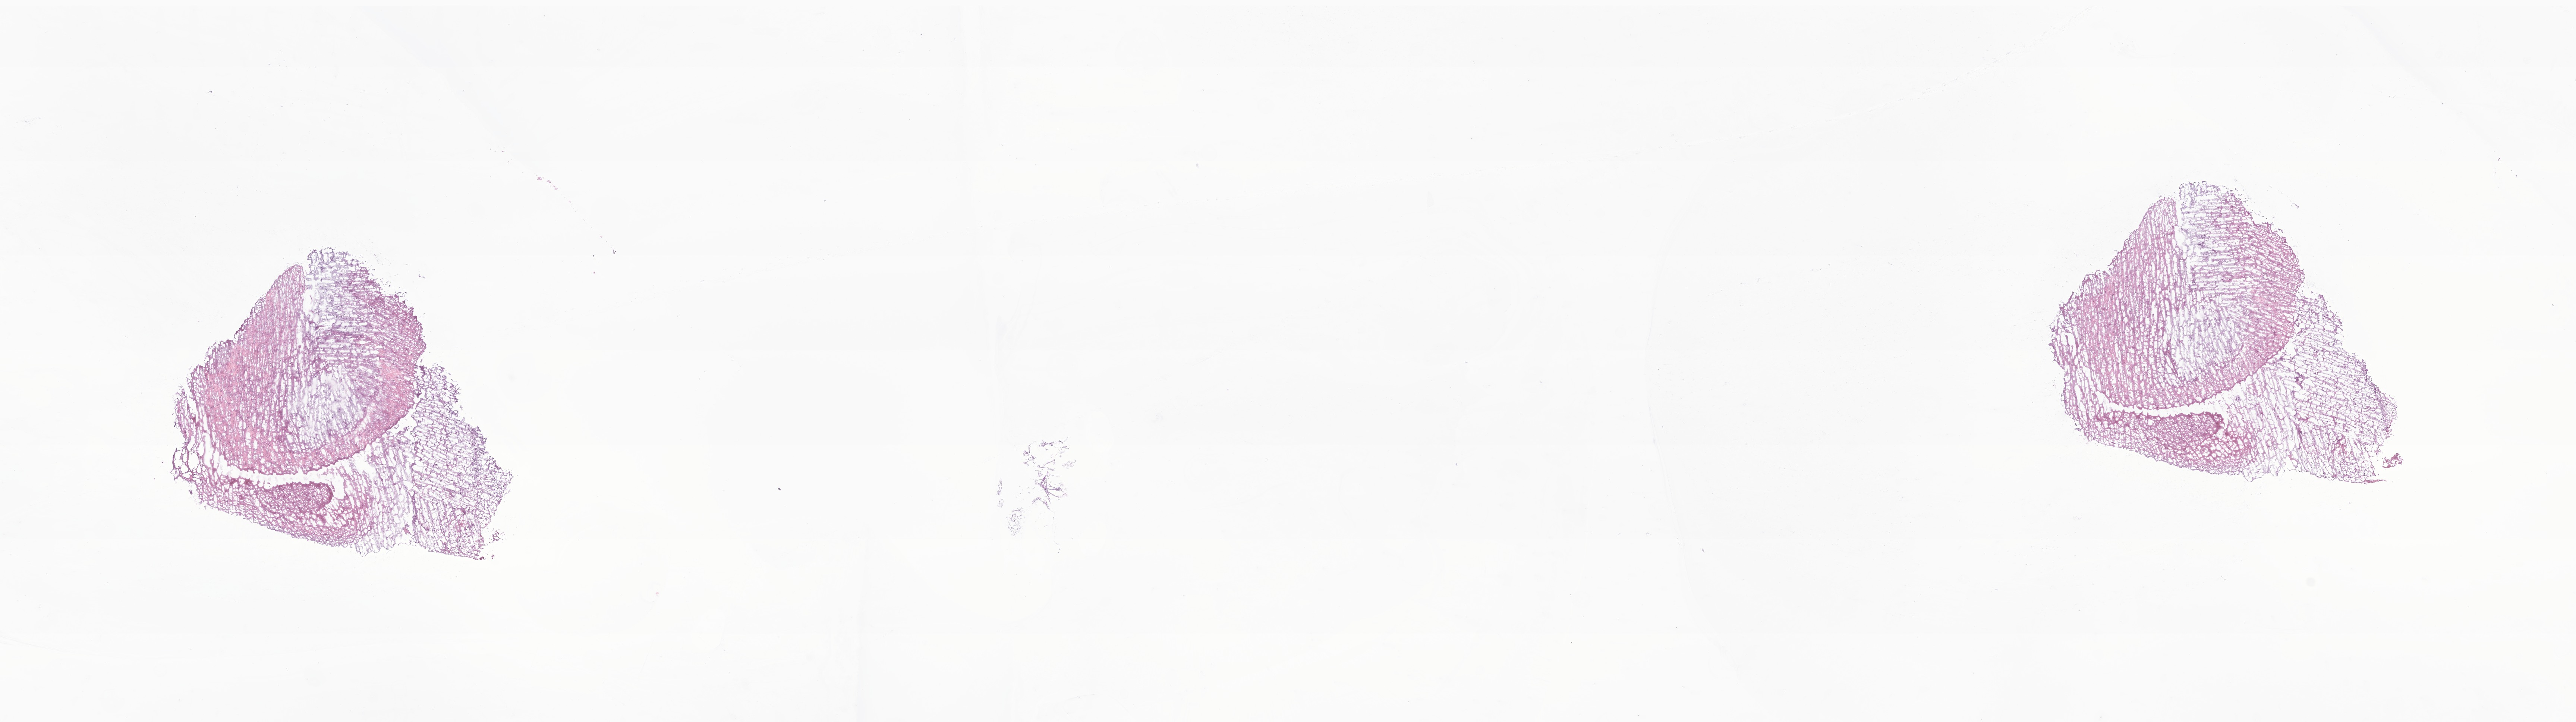
Digitized H&E-stained section of tumor tissue from the brain stem — a low-resolution overview of the entire scanned area, about 29.1 x 8.2 mm. Frozen section (OCT-embedded). Female patient, age 222 months (18 years 6 months).
Diagnosis (ICD-O-3 morphology term): Pilocytic astrocytoma.